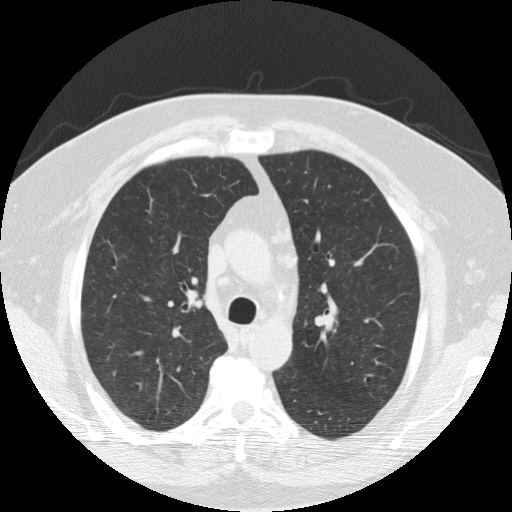
Chest CT (low-dose screening protocol), one axial image, second screening round (one year after baseline), lung window (W 1500 / L -600 HU), slice 77 of 227 in the series. Male, age 60 years at enrolment. Current smoker at enrolment.
Expert reader's lesion annotation, bounding box <314,307,341,337> (left, top, right, bottom; pixels). Screening reader's record for this exam: no non-calcified nodule ≥4 mm recorded.